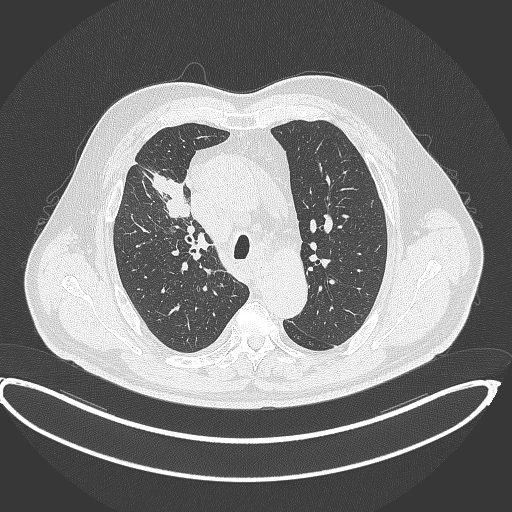
Chest CT, one axial slice; slice 288 of 390 in the series (ordered by position); 120 kVp; lung window (W 1500 / L -600 HU); 1 mm slice thickness; 512 × 512 image matrix, field of view 448 × 448 mm. Male patient, age 62 years. Case-level facts recorded for this patient, not image findings: clinical TNM (as recorded): T1c N3 M1c.
Annotated regions visible in this slice (rectangle marked by the reading radiologist):
- lung tumour (recorded histology: adenocarcinoma): bounding box (x1, y1, x2, y2) in pixels: (147, 167, 192, 219)